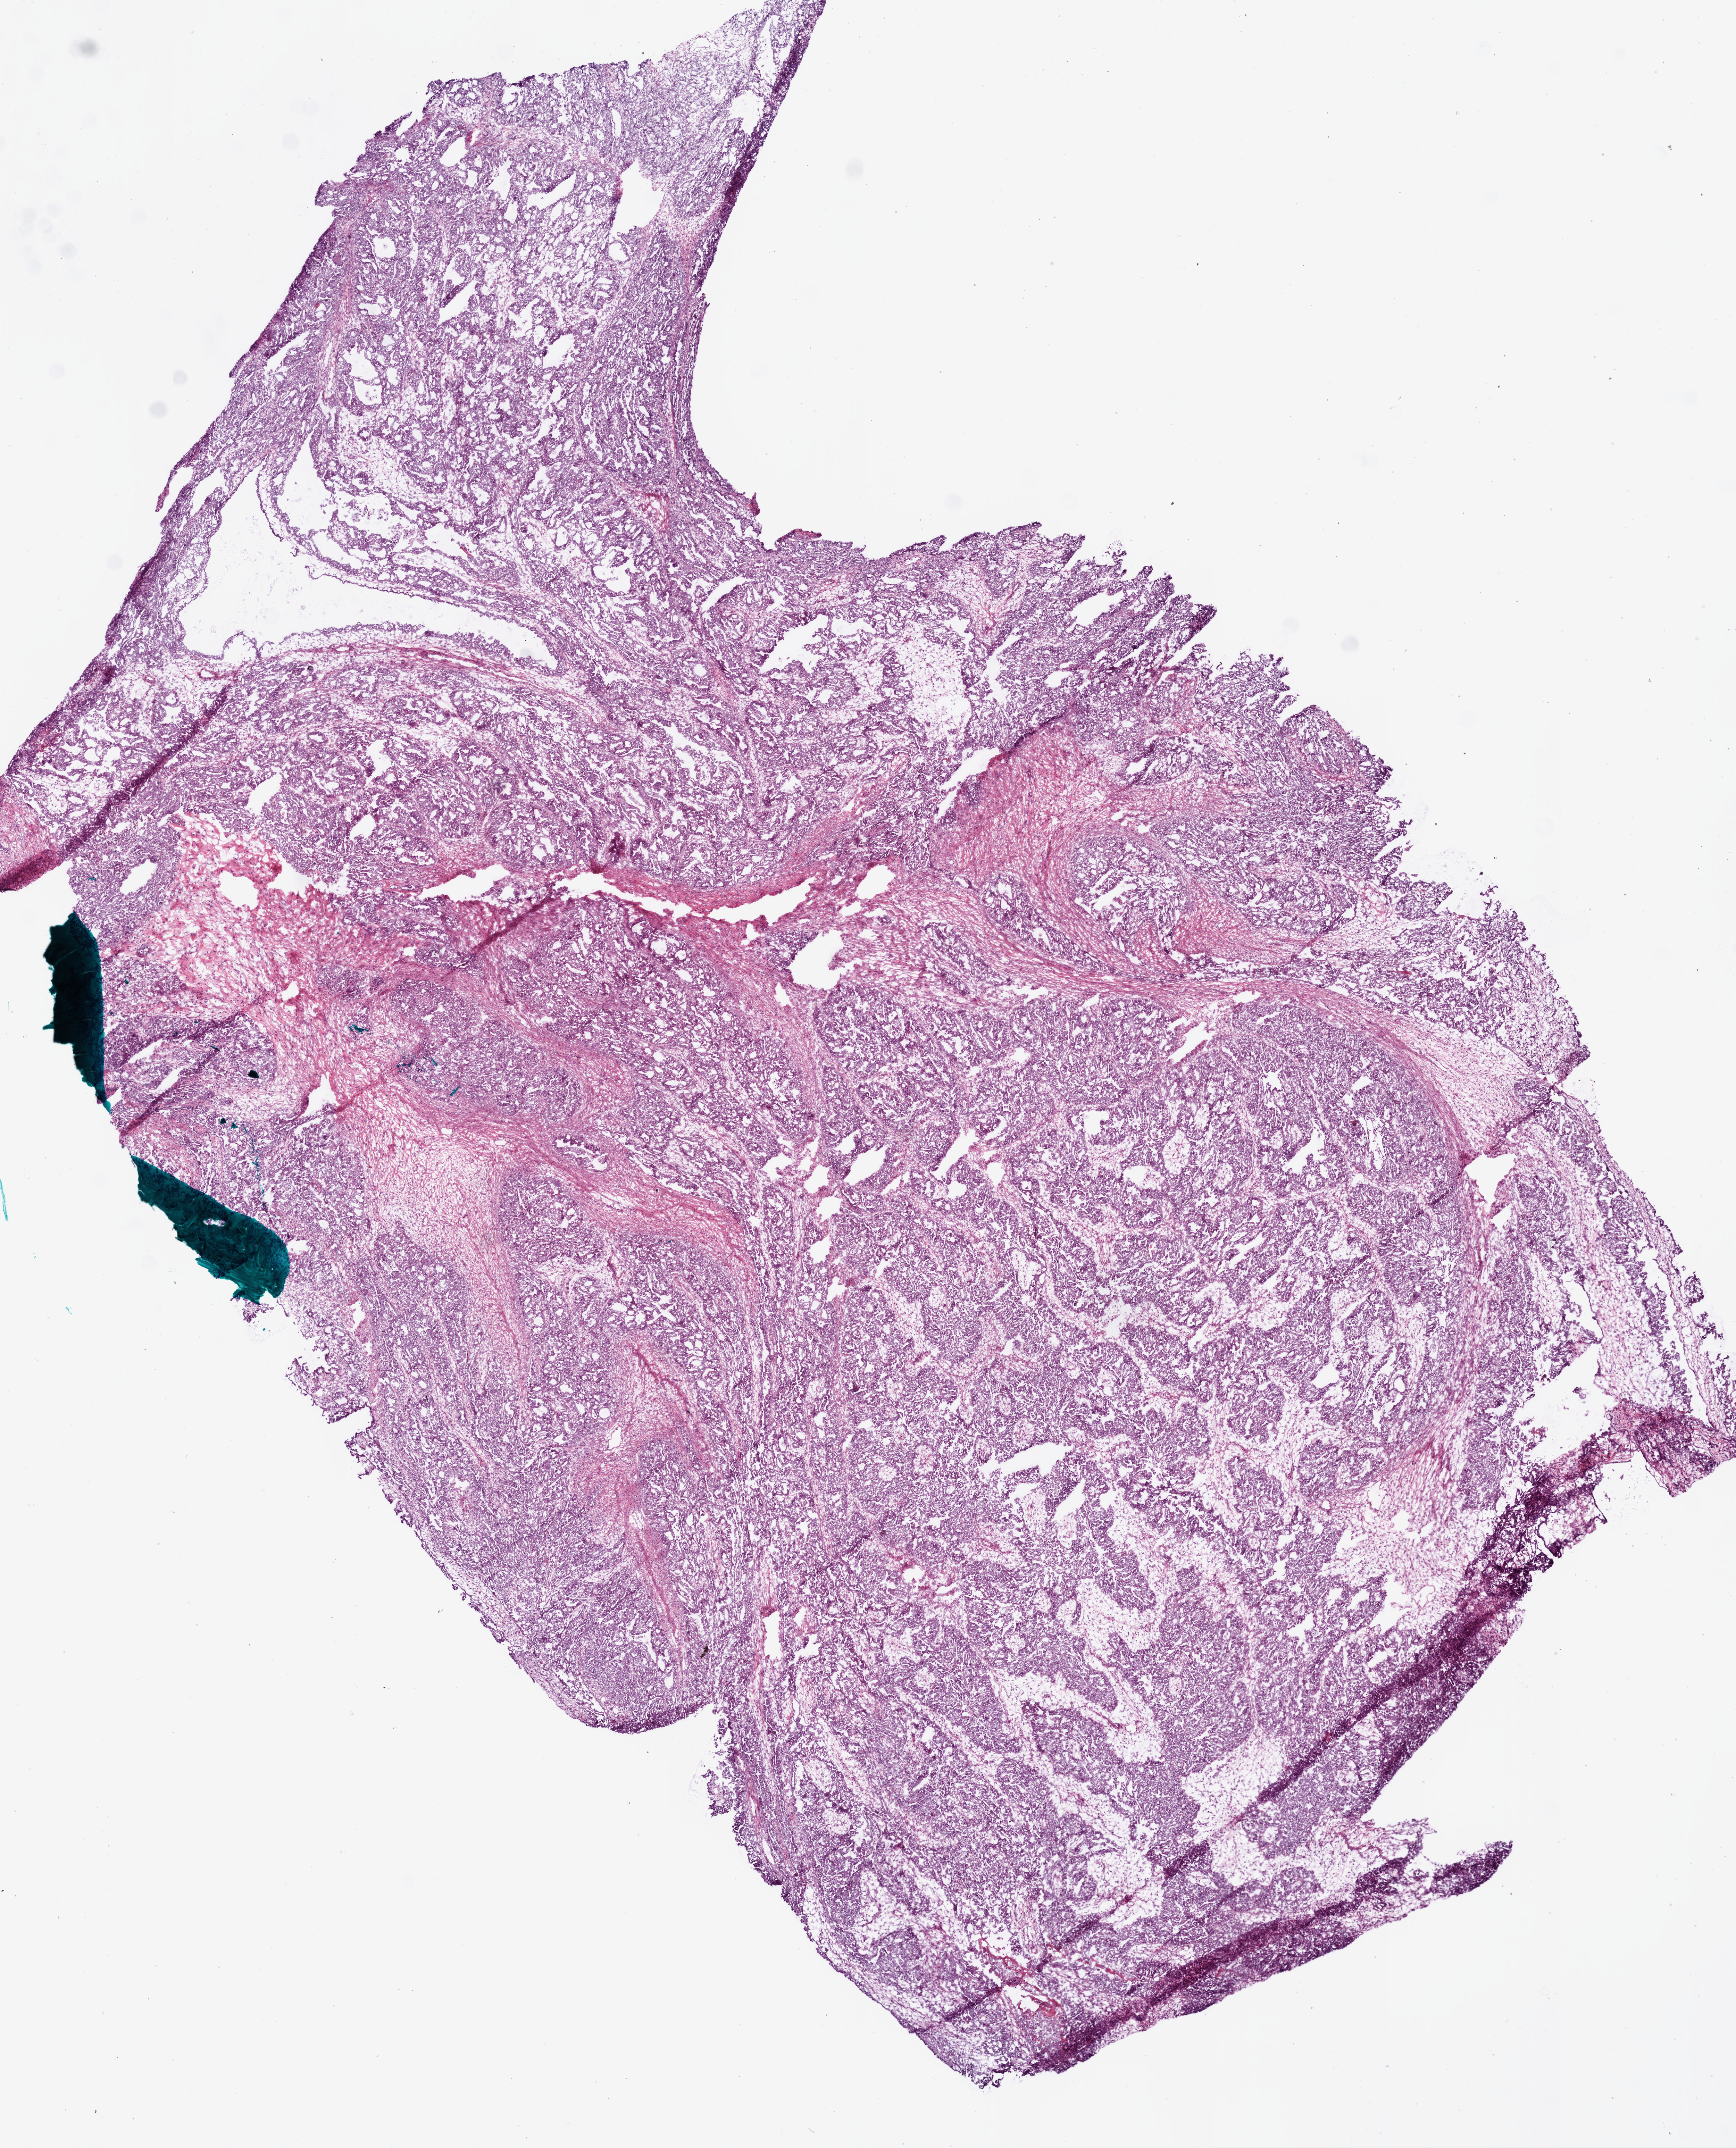
Hematoxylin and eosin (H&E) stained whole-slide image, whole scanned area (about 10.0 x 12.4 mm) shown as a low-resolution overview; frozen section from the bottom of the tissue portion; ovary, primary tumour sample. Female, age 34 years at initial diagnosis.
Diagnosis: Serous cystadenocarcinoma, NOS.